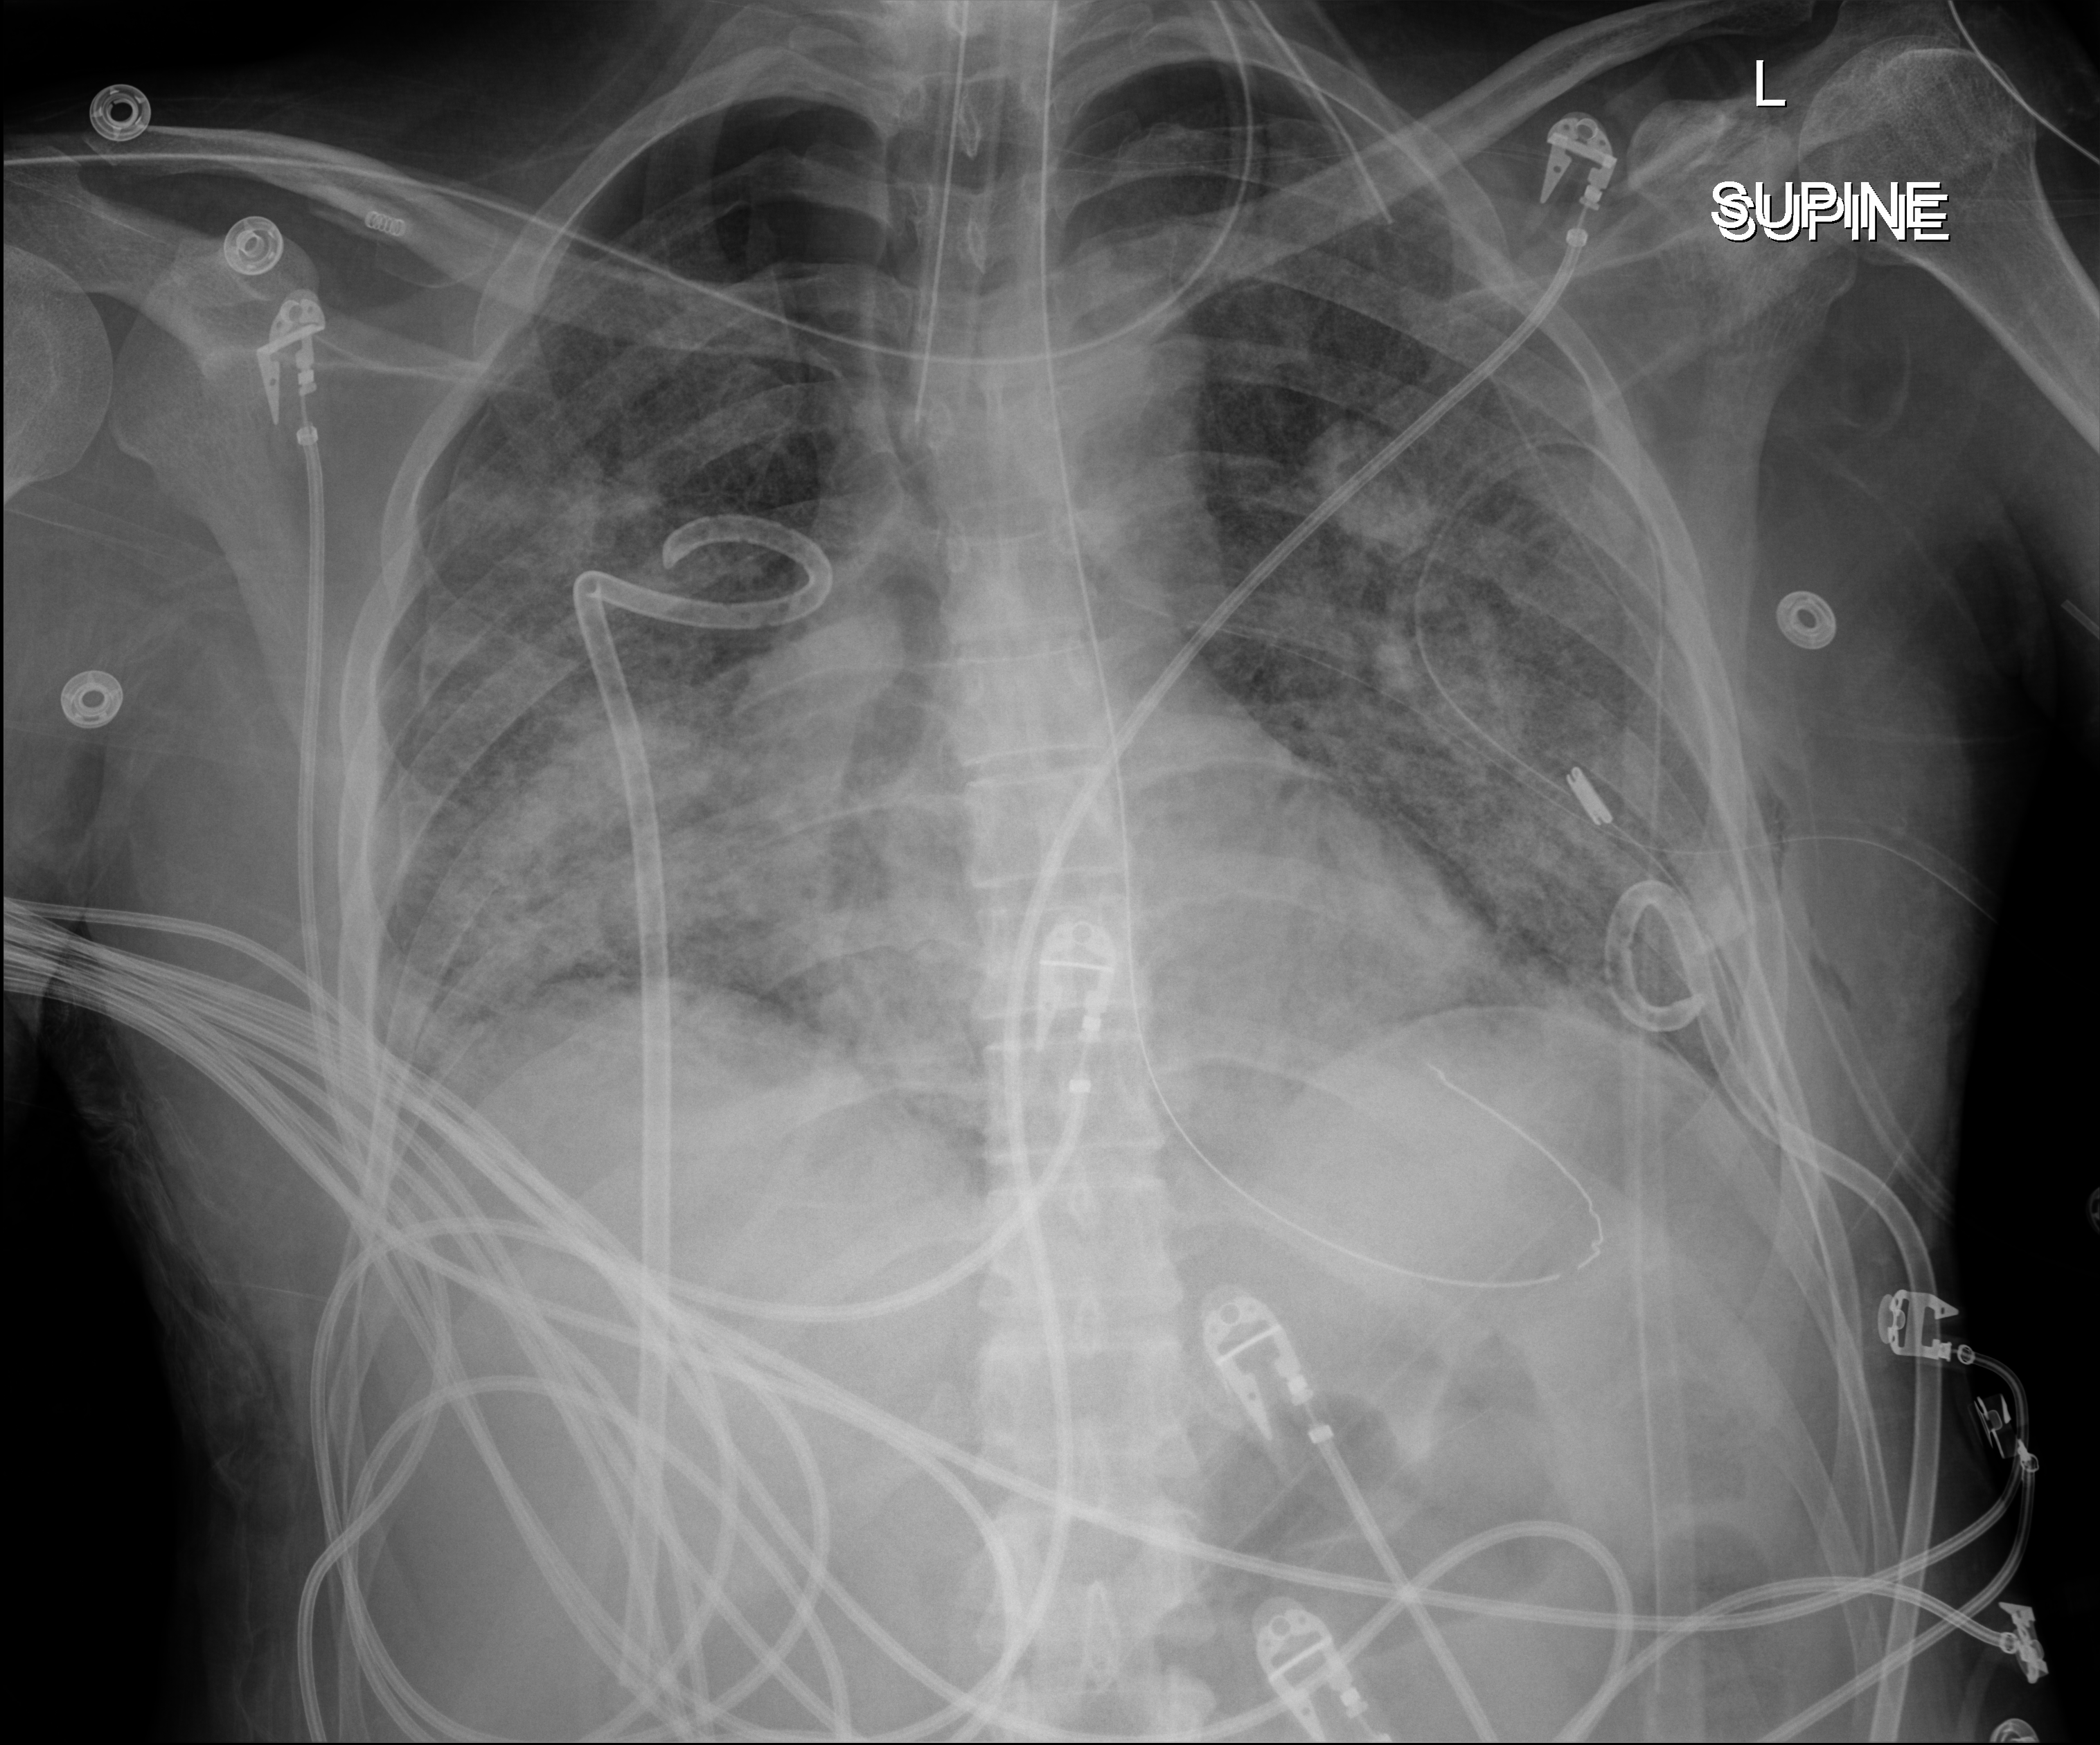
Chest radiograph (digital radiography). Patient hospitalised with COVID-19, aged 18–59 years.
From the hospital-stay record, not from the radiograph (when in the stay this image was taken is not recorded):
- admitted to intensive care during this hospital stay: yes